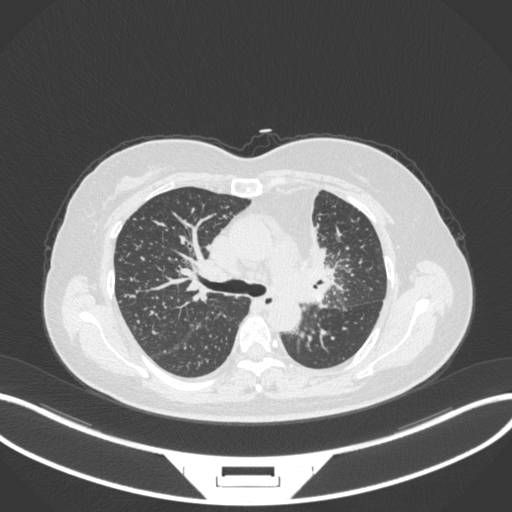
Chest CT, one axial slice; slice 216 of 348 in the series (ordered by position); reconstruction kernel B31f; 120 kVp; lung window (W 1500 / L -600 HU); 512 × 512 image matrix, field of view 400 × 400 mm. Patient: female, 49 years. Case-level facts recorded for this patient, not image findings: clinical TNM (as recorded): T1c N0 M1.
Annotated regions visible in this slice (bounding box drawn by a radiologist):
- lung tumour (recorded histology: adenocarcinoma): box from (x=285, y=207) to (x=338, y=311) px